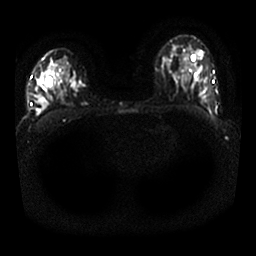
Breast MRI, one axial slice; position 15 of 25 along the scan axis; diffusion-weighted series; image 2 of 4 stored at this slice position (different b-values; order by instance number); 1.5 T; 4 mm slice thickness; 256 × 256 image matrix, field of view 330 × 330 mm. Female patient.
Annotated regions visible in this slice (expert manual segmentation):
- tumour on diffusion-weighted imaging: bounding box (x1, y1, x2, y2) in pixels: (71, 82, 86, 91)